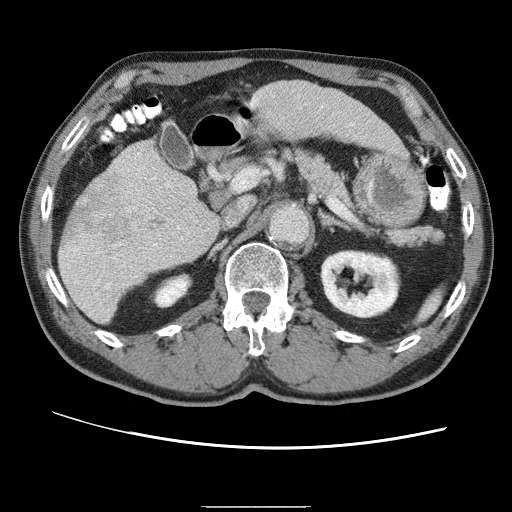
Contrast-enhanced abdominal CT (liver protocol), one axial slice. Slice 24 of 75 in the series (ordered by position). One of 2 acquisitions stored at this slice position. Soft-tissue window (W 400 / L 40 HU). 2.5 mm slice thickness. 512 × 512 image matrix, field of view 360 × 360 mm. From the clinical record (not read from this slice): diagnosis: hepatocellular carcinoma (patient treated with transarterial chemoembolisation; whether this scan precedes or follows treatment is not stated here); TNM stage (as recorded): Stage-II; Child-Pugh class: A; tumour differentiation: well differentiated.
Outlined on this slice (semi-automatic segmentation, software-assisted and operator-edited):
- liver parenchyma outside the tumour (the mass and vessels are separate outlines, so this box may not span the whole liver): bounding box <60,84,364,322> (left, top, right, bottom; pixels)
- liver vessels: <70,99,346,256>